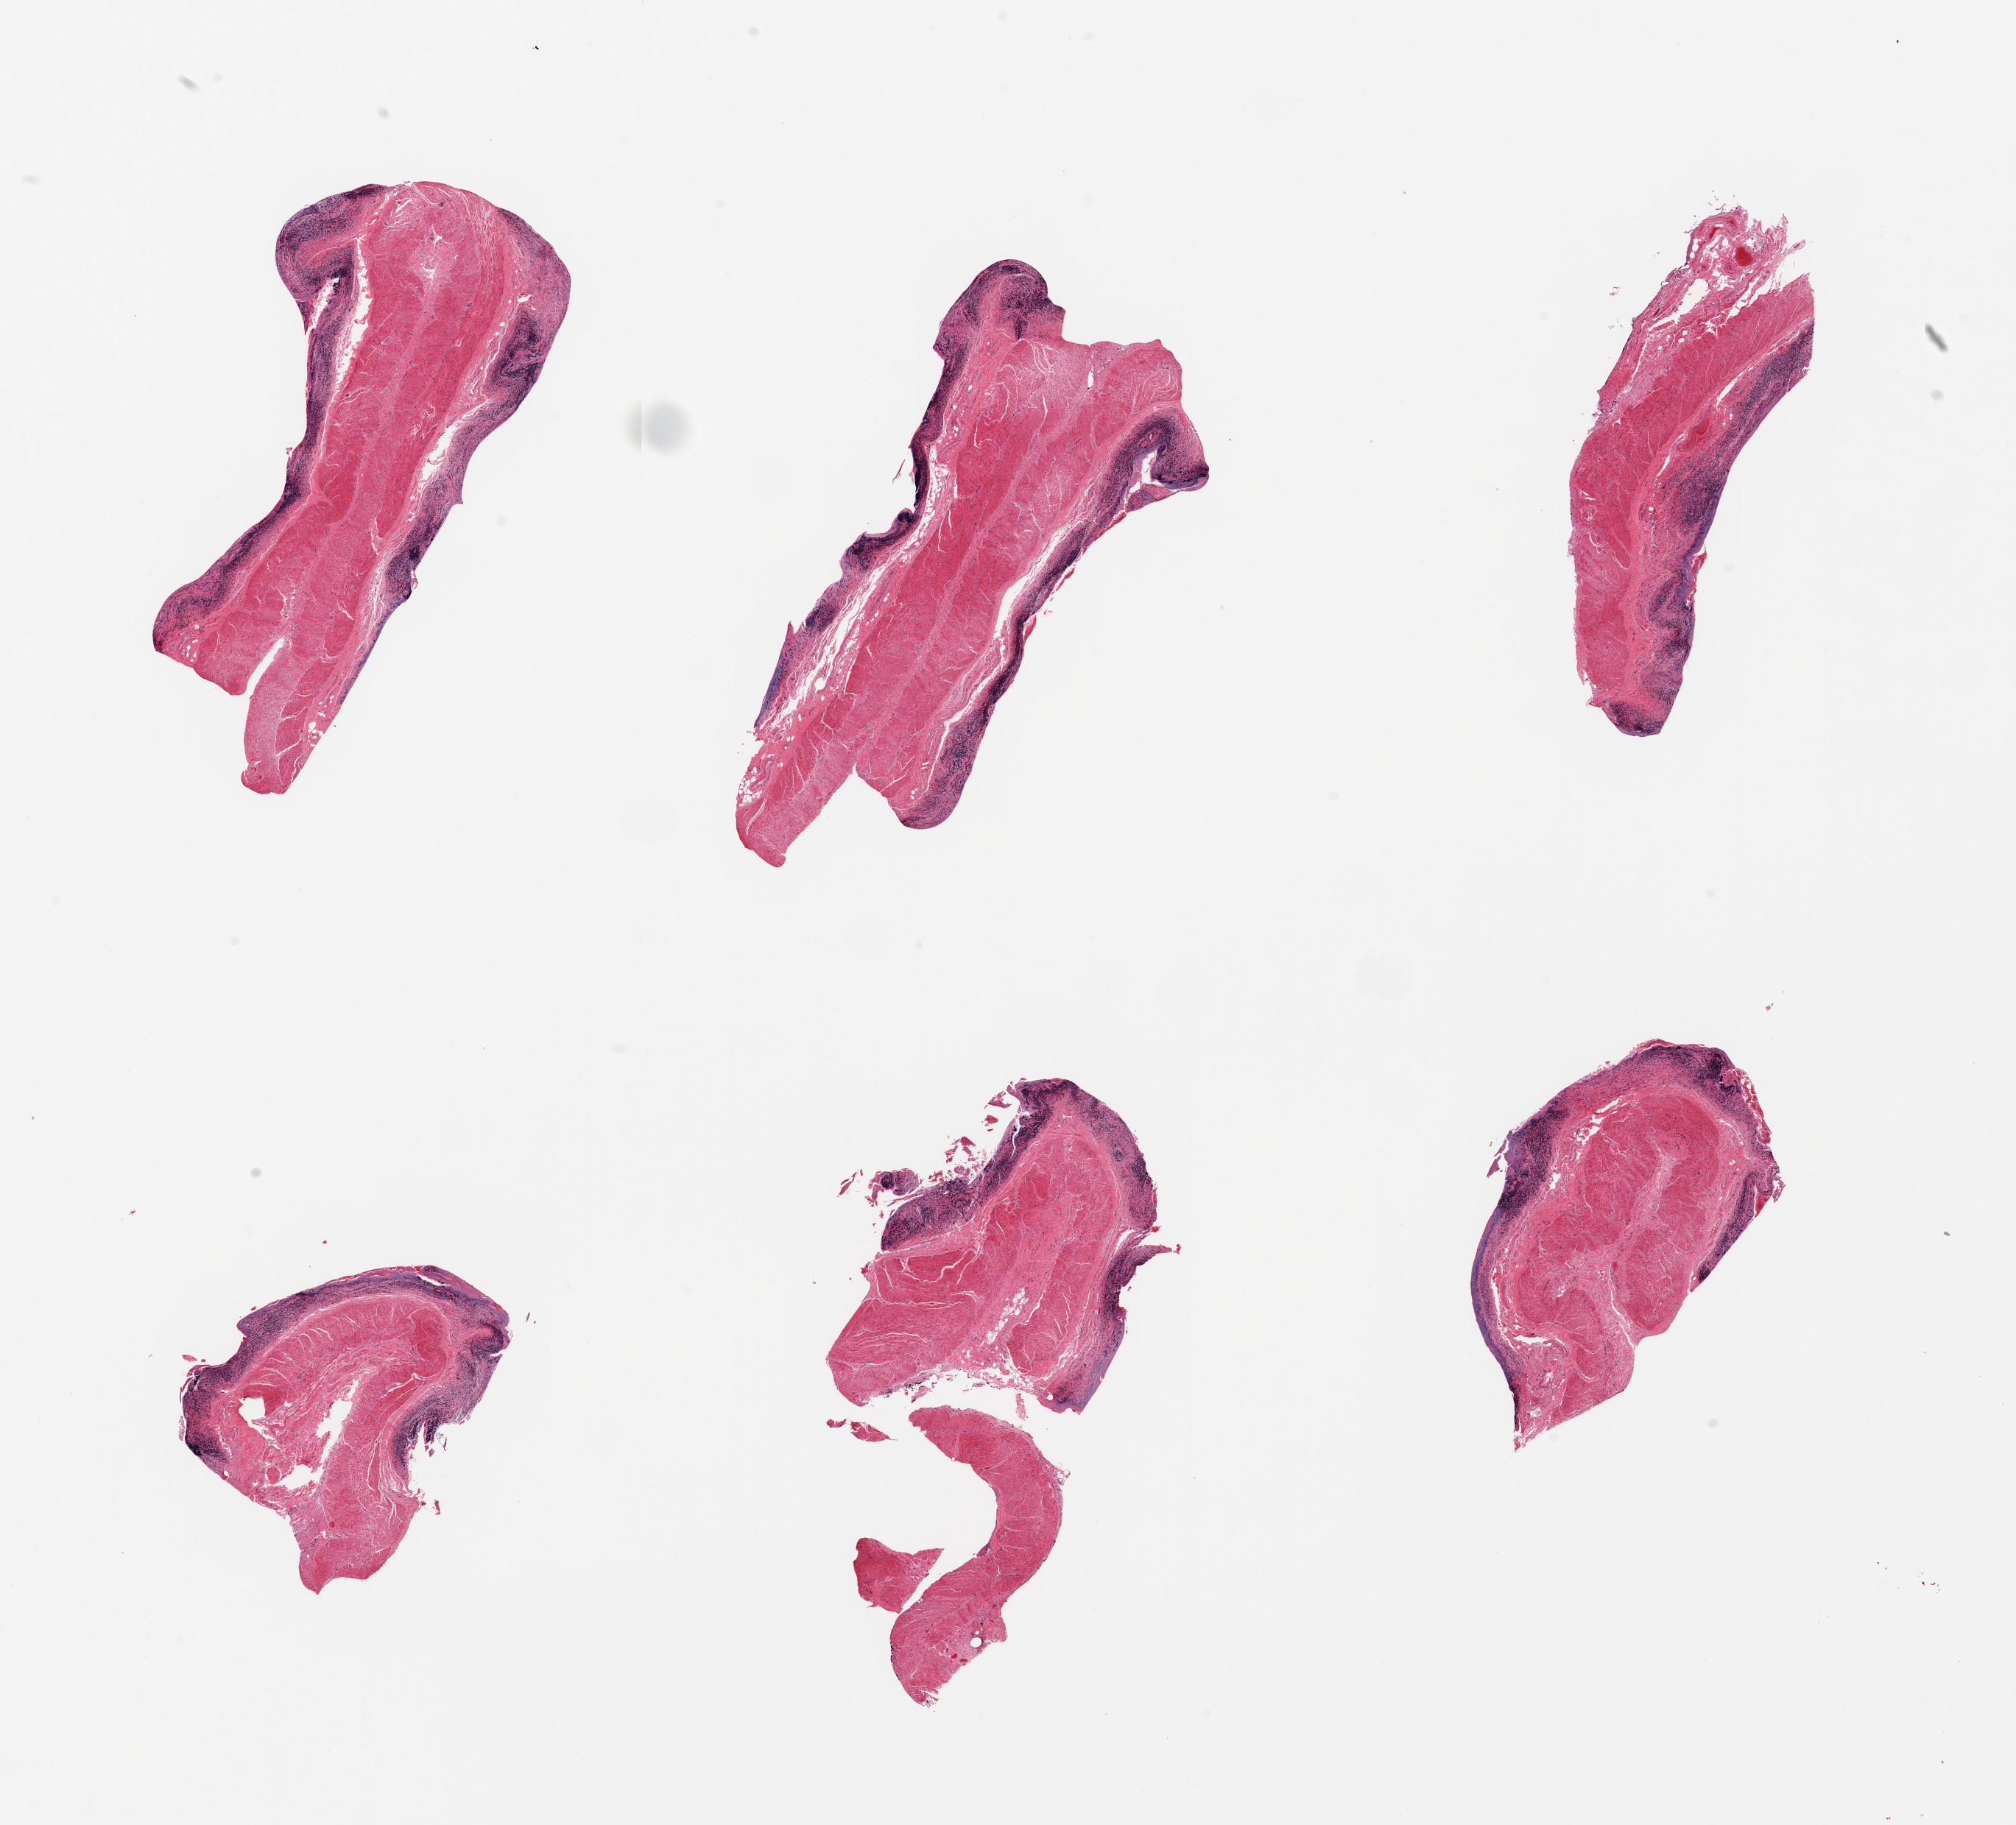
H&E whole-slide image — low-resolution overview of the scanned area, about 21.7 x 19.6 mm. Male donor.
Specimen: PAXgene-fixed paraffin-embedded (PFPE) section; section of ileum (target tissue); tissue donor sample.